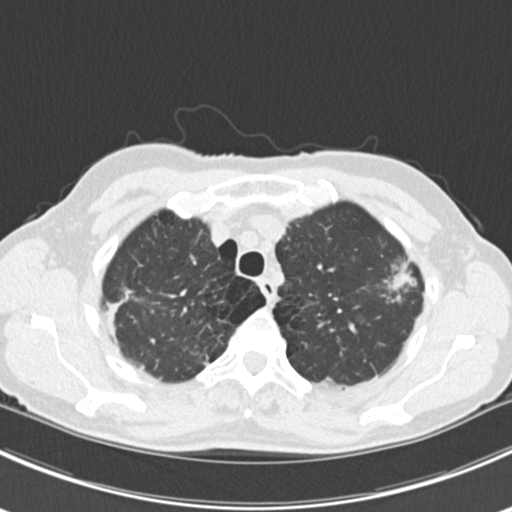
Low-dose screening chest CT, axial slice. Baseline annual screen. Lung window (W 1500 / L -600 HU). 2 mm slice thickness. Slice 38 of 224 in the series. Female participant, aged 63 years at enrolment. Current smoker at enrolment.
Expert-annotated lung lesion, bounding box <365,253,426,315> (left, top, right, bottom; pixels). The screening reader recorded 10 non-calcified nodules or masses ≥4 mm on this exam (right lower lobe, right lower lobe, left lower lobe, left lower lobe, right middle lobe, right lower lobe, left lower lobe, left upper lobe, right upper lobe, left upper lobe); which of them this box marks is not recorded. Official screen result: positive, change unspecified: nodule(s) >= 4 mm or enlarging nodule(s), mass(es), or other non-specific abnormalities suspicious for lung cancer. Lung cancer was diagnosed 751 days after this screen (after the third annual screen): bronchiolo-alveolar adenocarcinoma, NOS, right upper lobe, right middle lobe, right lower lobe, left upper lobe, left lower lobe, moderately differentiated (G2), stage IV (AJCC 6th edition).